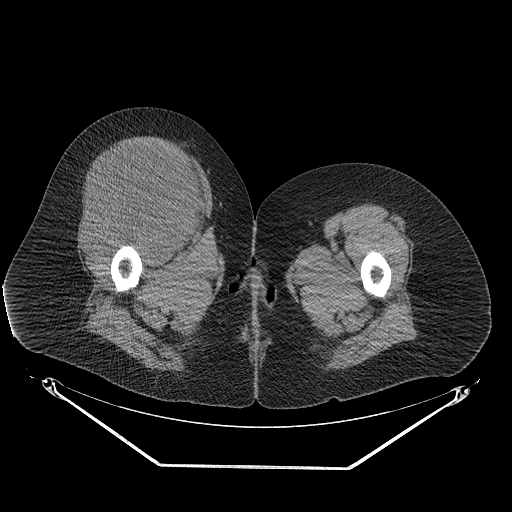
CT of an extremity soft-tissue mass (from a PET/CT study), one axial slice; position 46 of 267 along the scan axis; reconstruction kernel STANDARD; 140 kVp; soft-tissue window (W 400 / L 40 HU); 3.75 mm slice thickness; 512 × 512 image matrix, field of view 500 × 500 mm. Female patient. Case-level facts recorded for this patient, not image findings: histological type: malignant solitary fibrous tumor; grade: intermediate; site of the primary tumour: right thigh.
Annotated regions visible in this slice (expert contour drawn on MRI and transferred to this co-registered scan by the dataset authors):
- gross tumour volume including surrounding oedema: bounding box [x1, y1, x2, y2] px = [77, 144, 207, 243]
- gross tumour volume (mass): [82, 144, 204, 241]